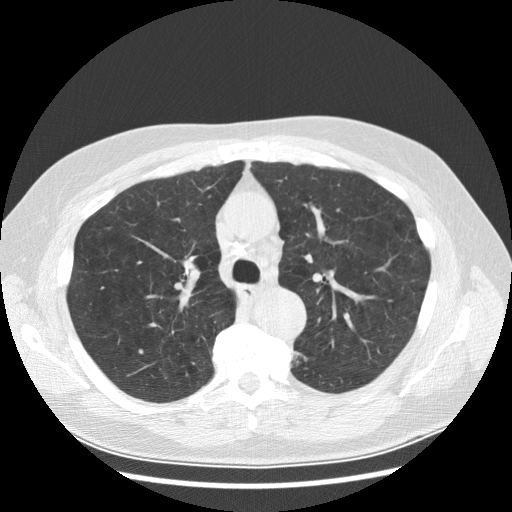
Low-dose screening chest CT, one axial slice. Position 197 of 282 along the scan axis. Reconstruction kernel STANDARD. 120 kVp. Lung window (W 1500 / L -600 HU). 2.5 mm slice thickness. 512 × 512 image matrix, field of view 370 × 370 mm.
Annotated regions visible in this slice (manually delineated by an expert):
- lesion 1 (tumor, lower lobe of left lung): bounding box (x1, y1, x2, y2) in pixels: (294, 351, 308, 365)